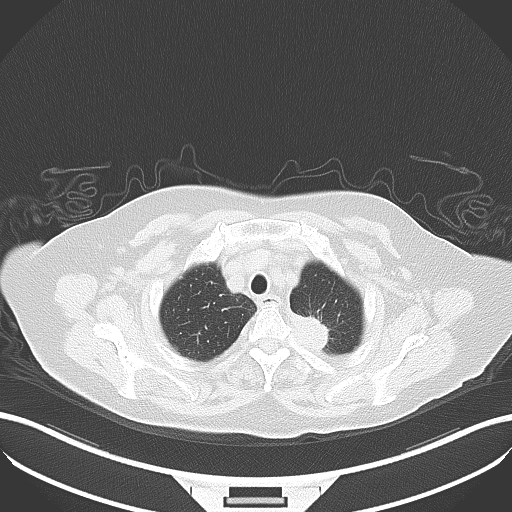
Chest CT, one axial slice; position 42 of 50 along the scan axis; reconstruction kernel B80f; 100 kVp; lung window (W 1500 / L -600 HU); 512 × 512 image matrix, field of view 400 × 400 mm. Female patient, age 81 years. Case-level facts recorded for this patient, not image findings: clinical TNM (as recorded): T2a N0 M0.
Annotated regions visible in this slice (rectangle marked by the reading radiologist):
- lung tumour (recorded histology: adenocarcinoma): bounding box [x1, y1, x2, y2] px = [291, 308, 333, 360]